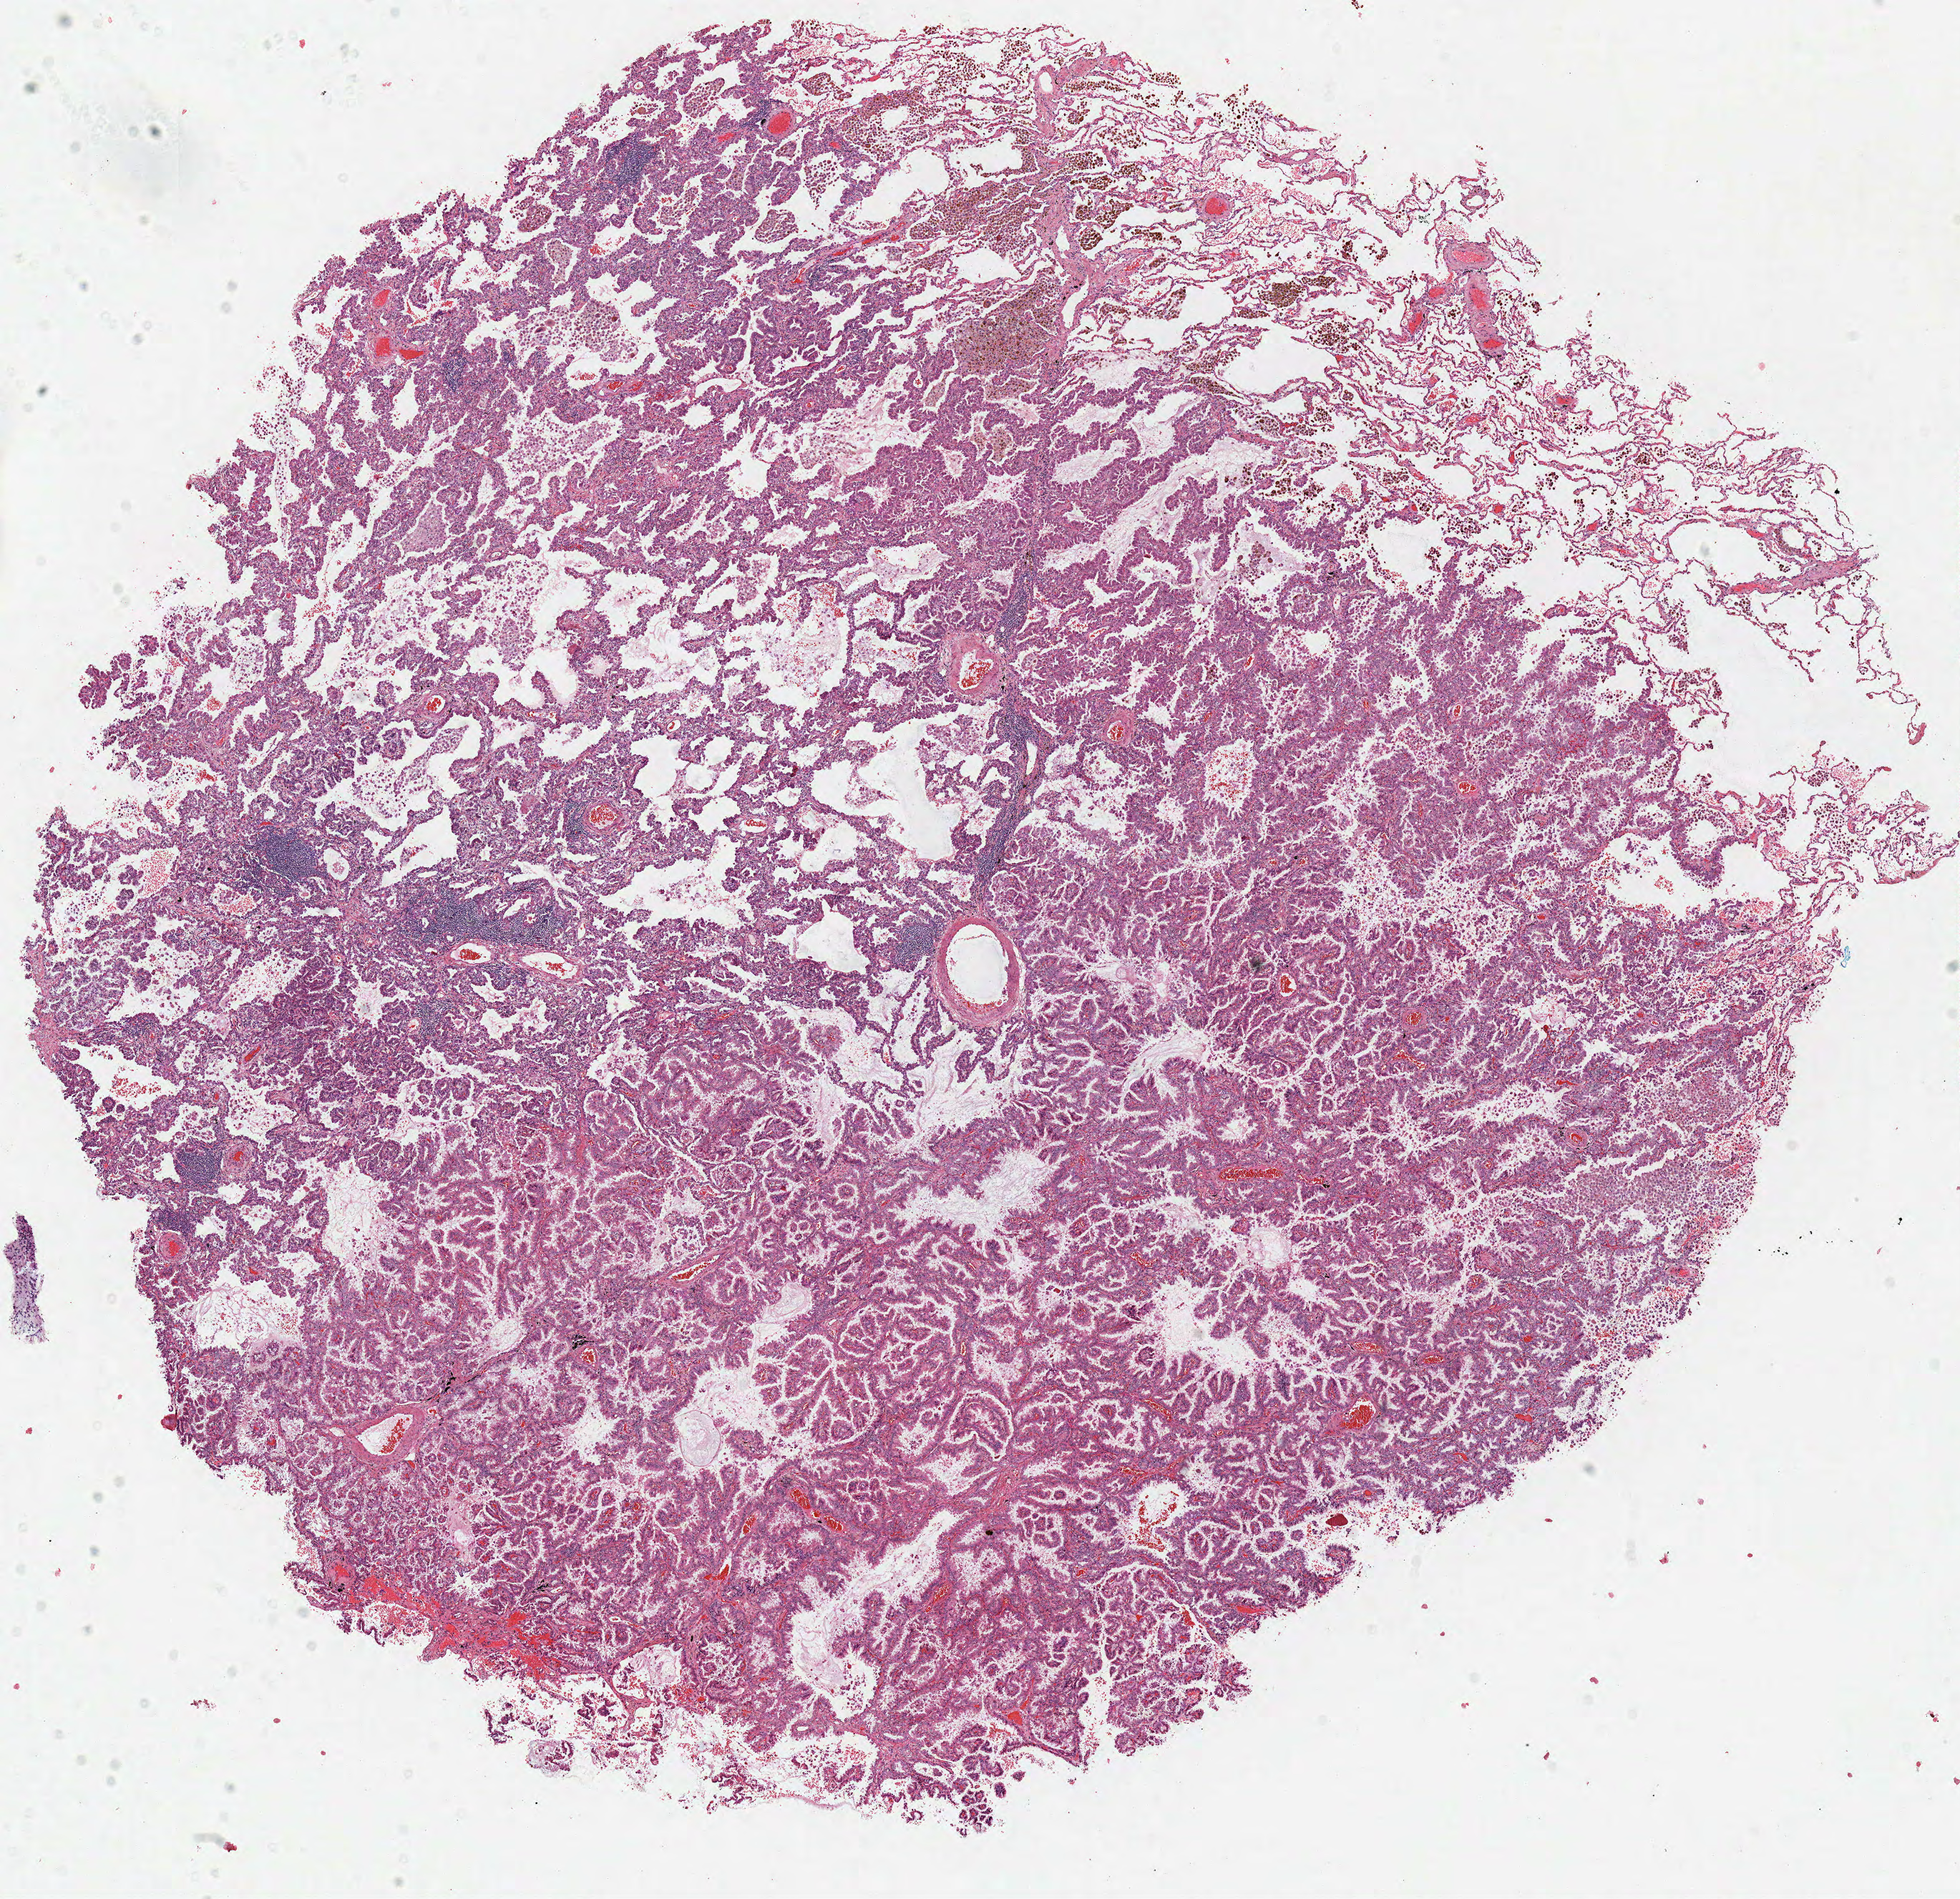
H&E-stained whole-slide image, a low-resolution overview of the entire scanned area, about 10.8 x 10.4 mm (acquisition: 40x scan), frozen section from the top of the tissue portion, sample: primary tumour, lung. Patient: female, age at initial diagnosis 60 years. Slide review estimates, as recorded: tumour cells 100%, tumour nuclei 85%, normal cells 0%, stromal cells 0%, necrosis 0%. Inflammatory infiltration, as recorded: lymphocyte infiltration 5%, monocyte infiltration 5%, neutrophil infiltration 0%.
AJCC pathologic stage: IA (6th edition). Histologic diagnosis: Adenocarcinoma, NOS (upper lobe, lung).